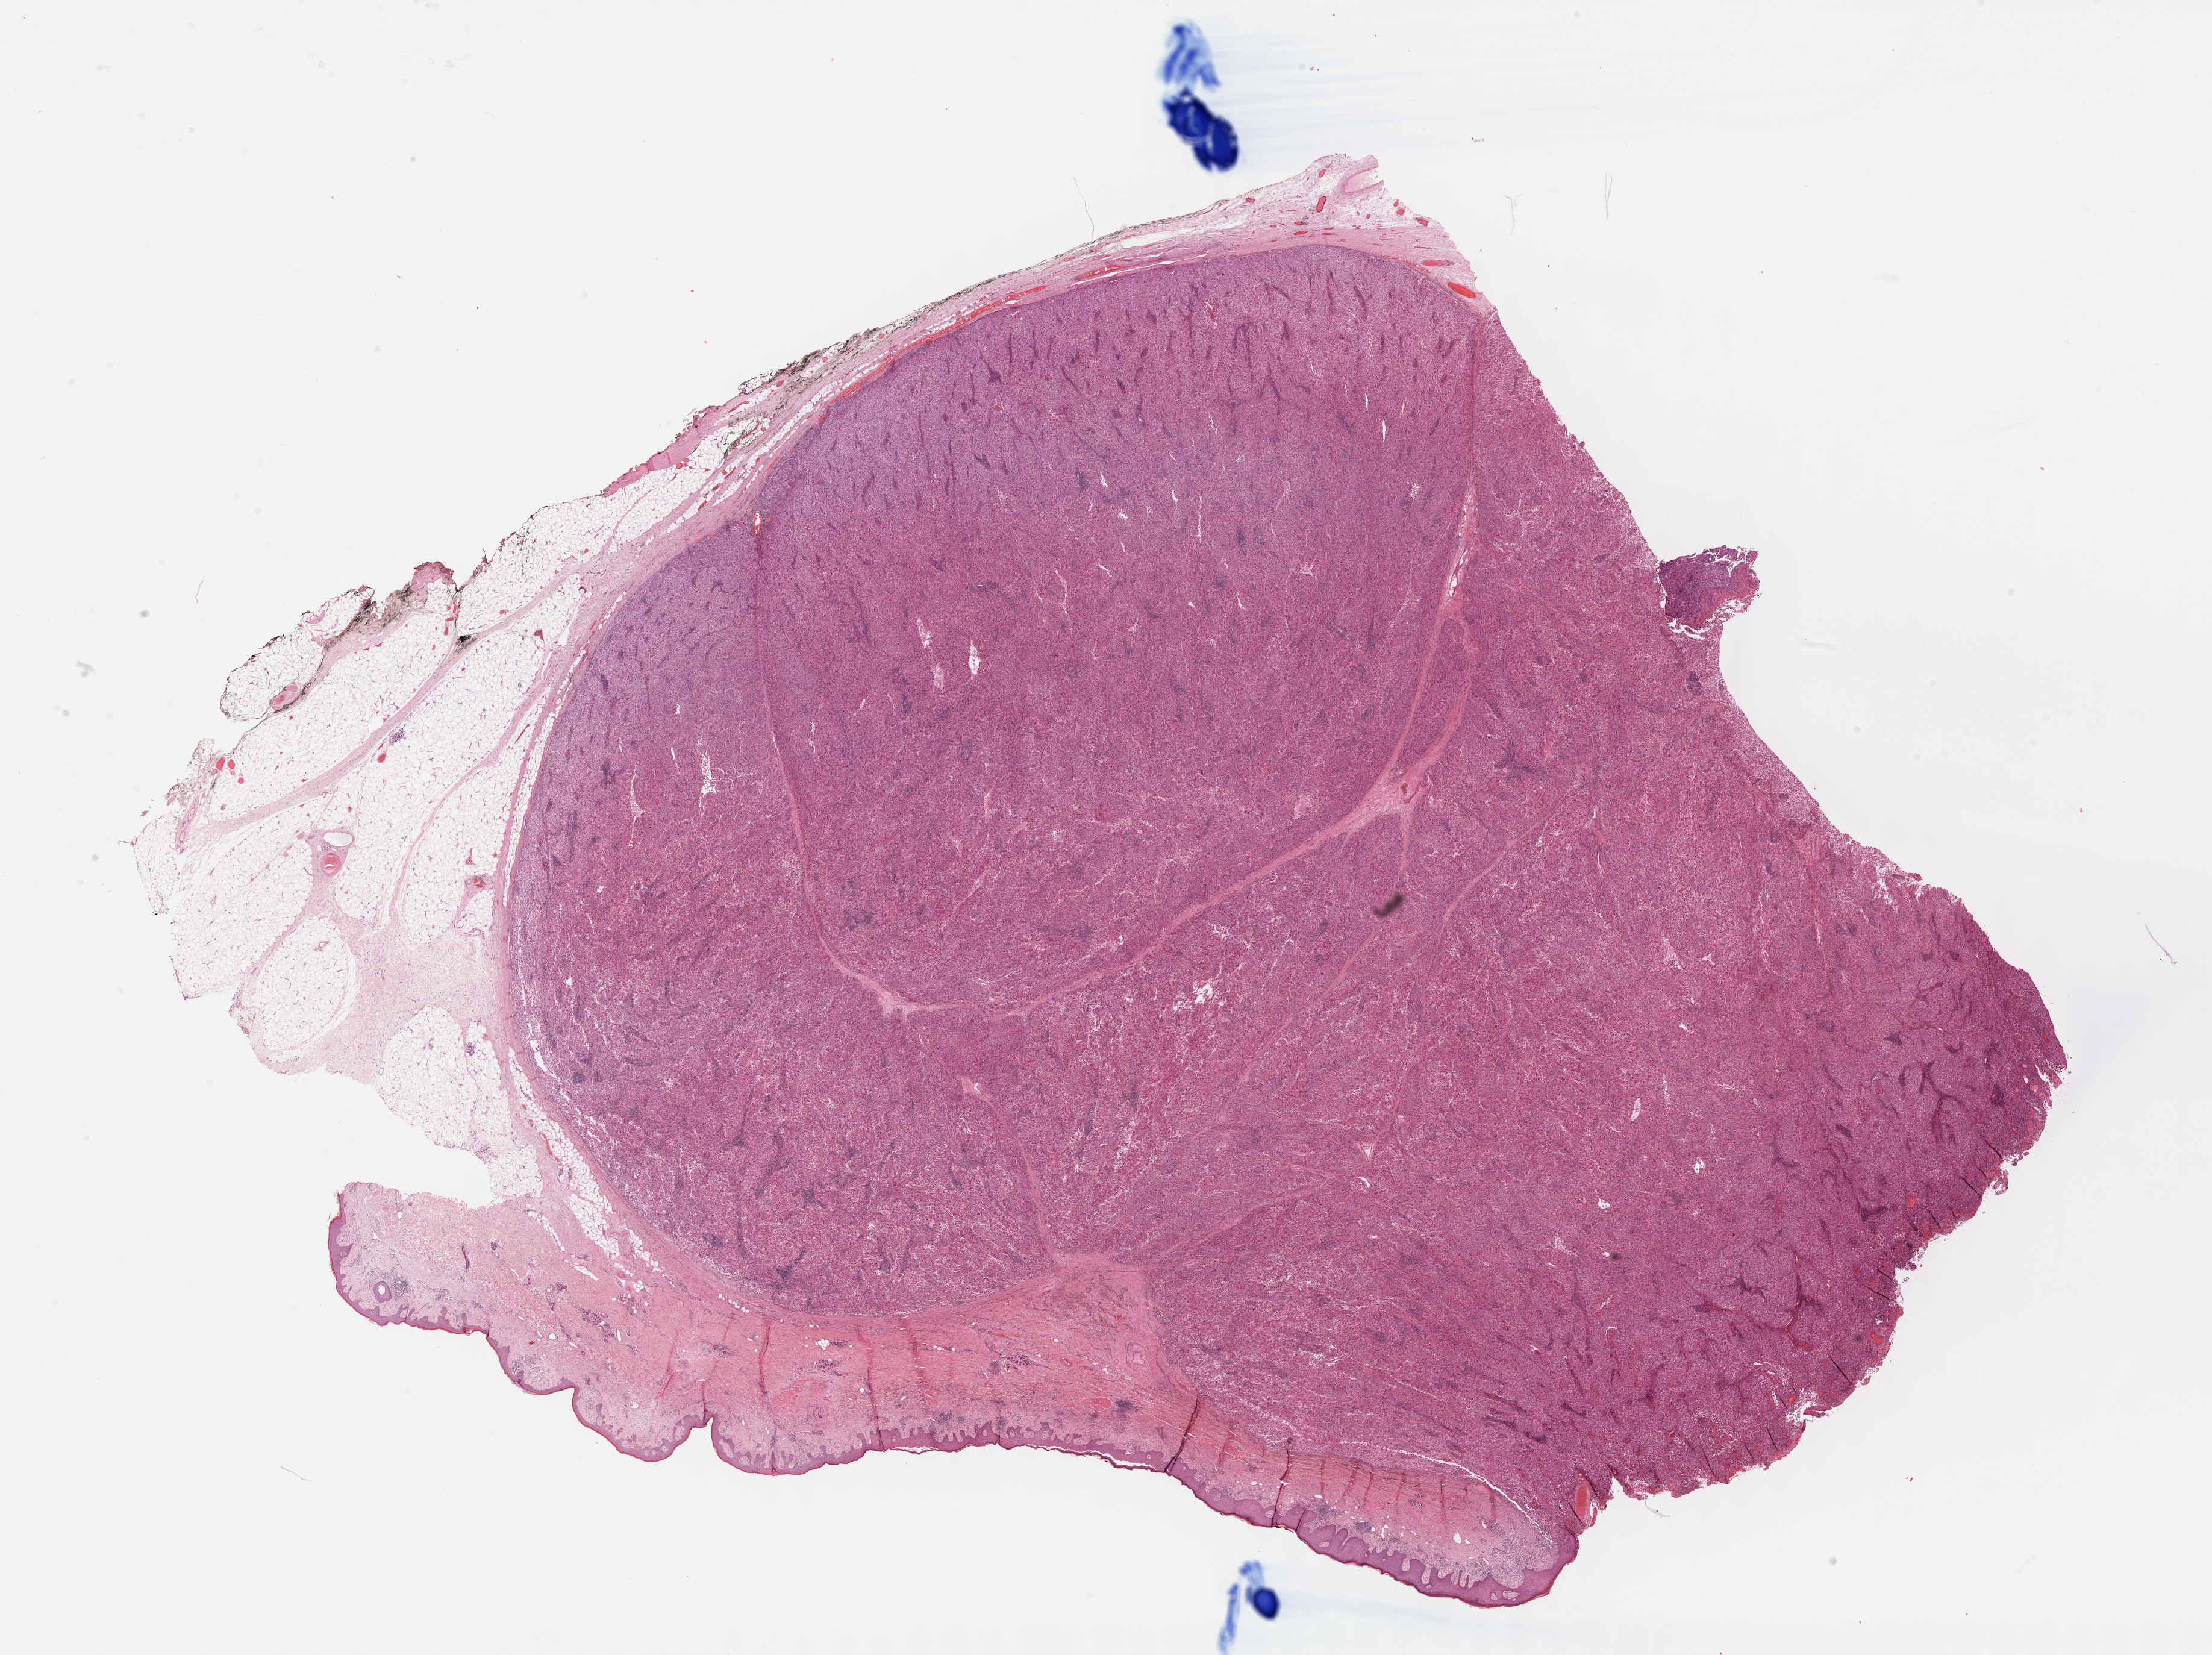
Digitized H&E-stained tissue section (whole slide), low-resolution overview of the scanned area, about 29.7 x 22.2 mm; formalin-fixed paraffin-embedded (FFPE) diagnostic section; sample: primary tumour, skin. Male, age 85 years at initial diagnosis.
Pathologic diagnosis: Nodular melanoma.